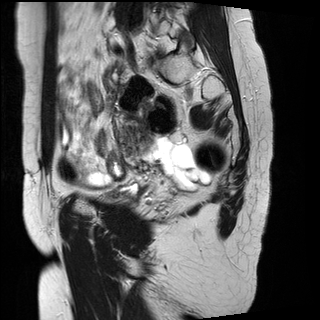
Pelvic MRI for cervical cancer, one sagittal slice; position 21 of 29 along the scan axis; T2-weighted; 1.5 T; TE 89 ms, TR 2930 ms; 320 × 320 image matrix. Patient: female, 45 years.
Annotated regions visible in this slice (manually delineated by an expert):
- uterus and cervix: bounding box [x1, y1, x2, y2] px = [123, 117, 152, 156]